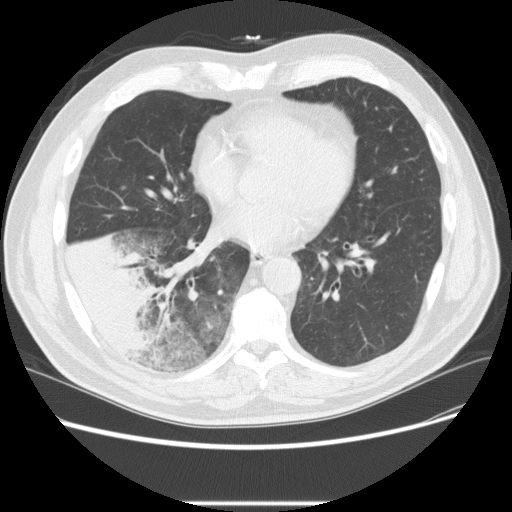
Low-dose screening chest CT, one axial slice; position 96 of 233 along the scan axis; 120 kVp; lung window (W 1500 / L -600 HU); 2.5 mm slice thickness; 512 × 512 image matrix.
Outlined on this slice (manually delineated by an expert):
- lesion 3 (tumor, lower lobe of right lung): bounding box [x1, y1, x2, y2] px = [68, 232, 162, 349]